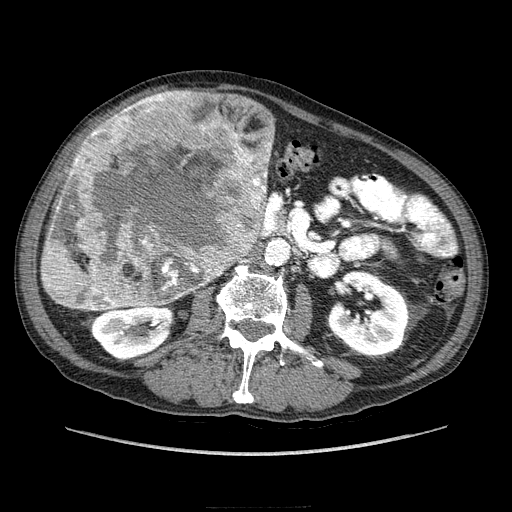
Contrast-enhanced abdominal CT (liver protocol), one axial slice; position 85 of 218 along the scan axis; 100 kVp; soft-tissue window (W 400 / L 40 HU); 512 × 512 image matrix, field of view 380 × 380 mm. From the clinical record (not read from this slice): diagnosis: hepatocellular carcinoma (patient treated with transarterial chemoembolisation; whether this scan precedes or follows treatment is not stated here); TNM stage (as recorded): Stage-IIIA; Child-Pugh class: A; tumour size: 20 cm.
Annotated regions visible in this slice (semi-automatically segmented with operator editing):
- liver parenchyma outside the tumour (the mass and vessels are separate outlines, so this box may not span the whole liver): bounding box <70,135,270,173> (left, top, right, bottom; pixels)
- mass: <40,89,274,312>